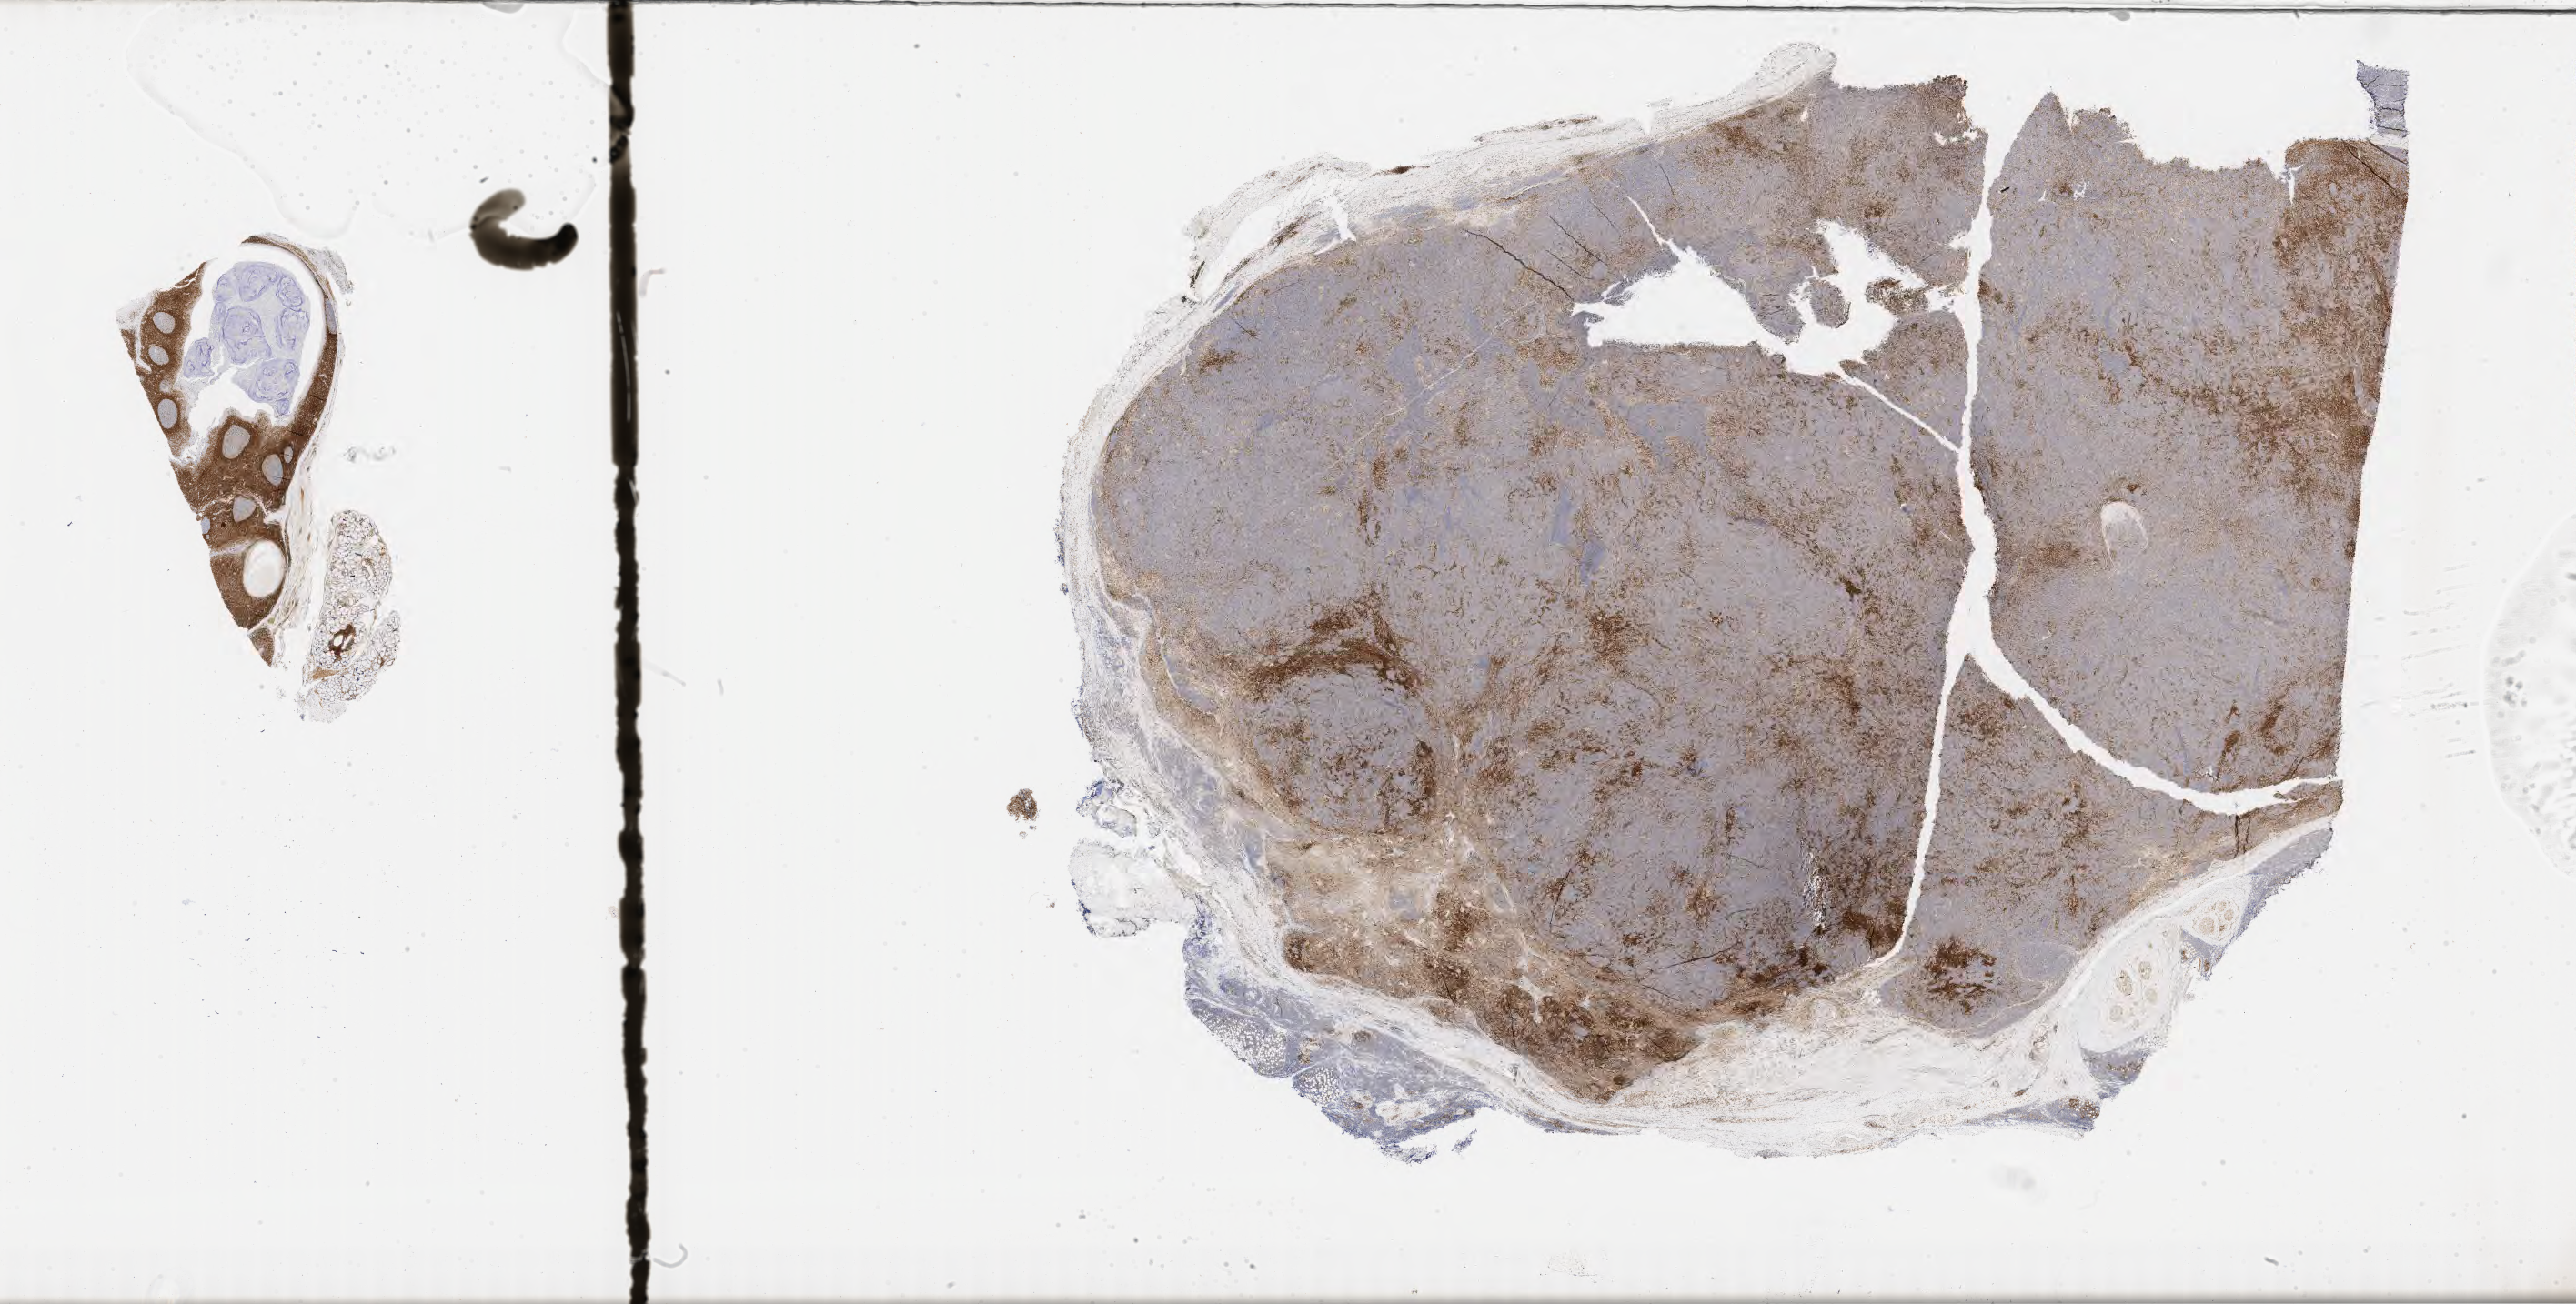
Whole-slide image, immunohistochemical stain for BCL2, whole scanned area (about 45.8 x 23.2 mm) shown as a low-resolution overview. Tumor tissue. Male patient, age 30 years.
- histologic diagnosis: Burkitt lymphoma, NOS